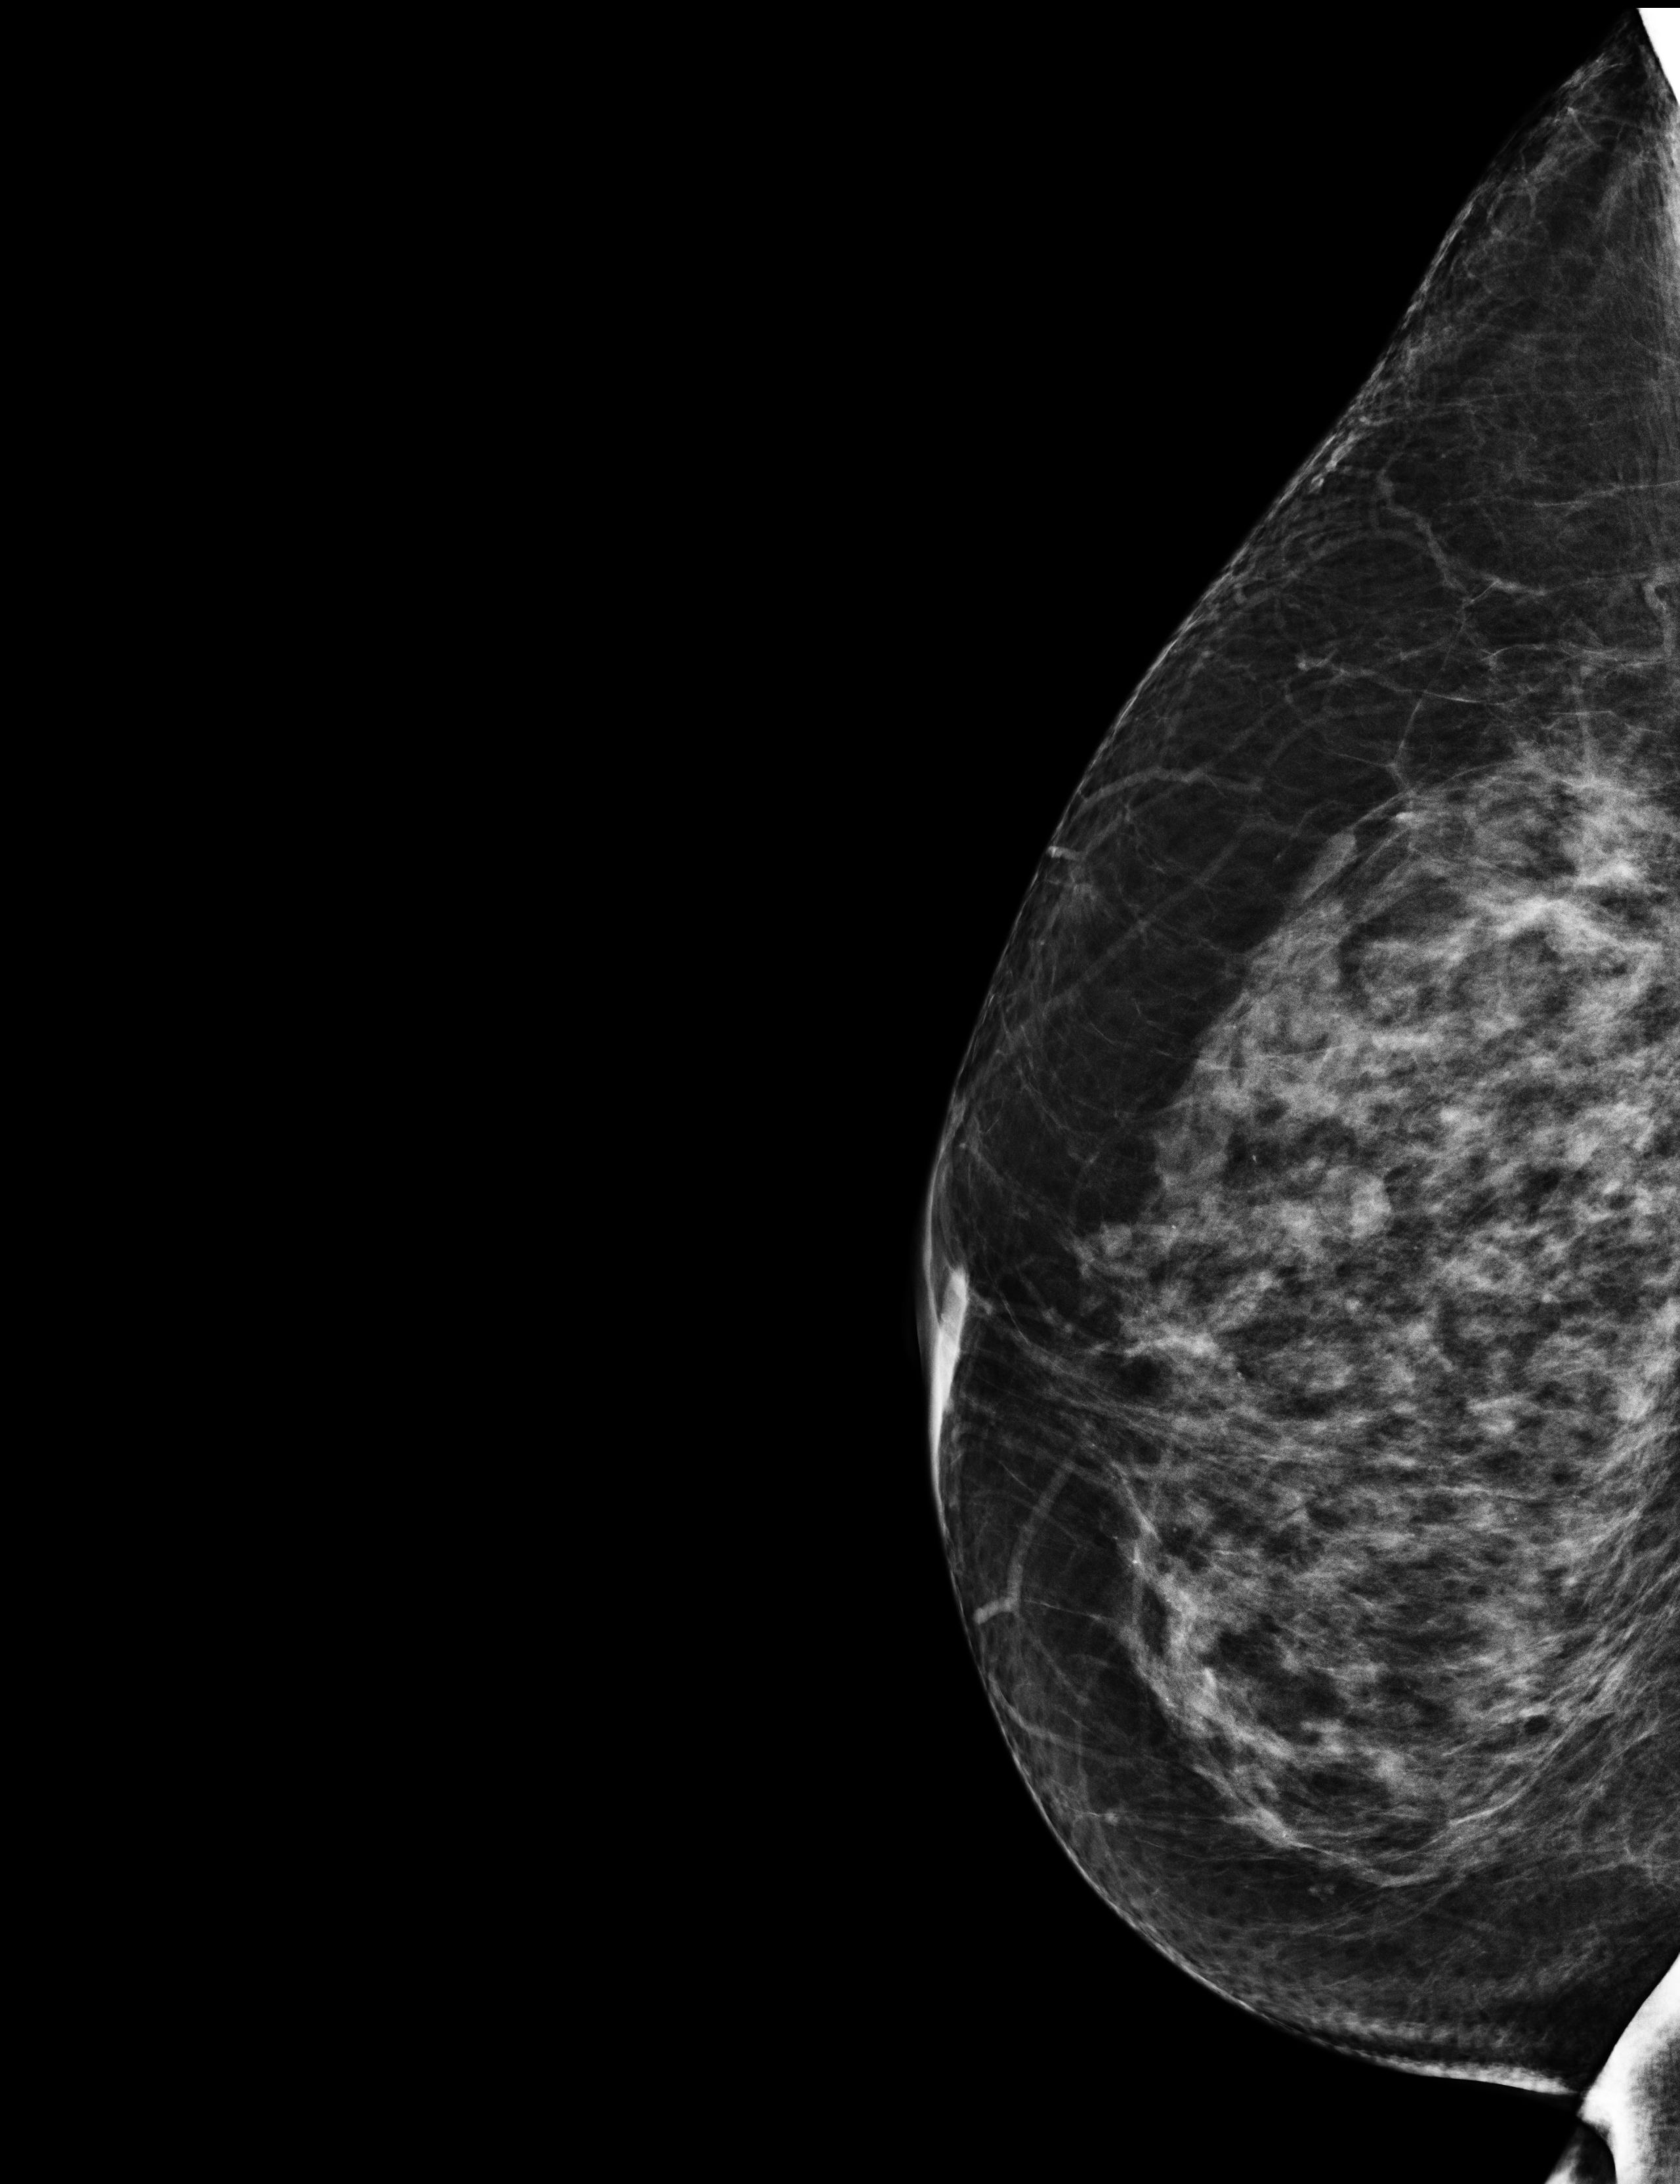
Full-field digital mammogram (FFDM); right breast; mediolateral oblique (MLO) view; screening examination; compressed breast thickness 67 mm; system: Selenia Dimensions. Patient aged 70 years (female).
BI-RADS breast density category at the screening exam (both breasts, scale 1–4): 3. Final BI-RADS category for the screening round (tomosynthesis exam, both breasts): category 2. Recall: no recall after this screen.